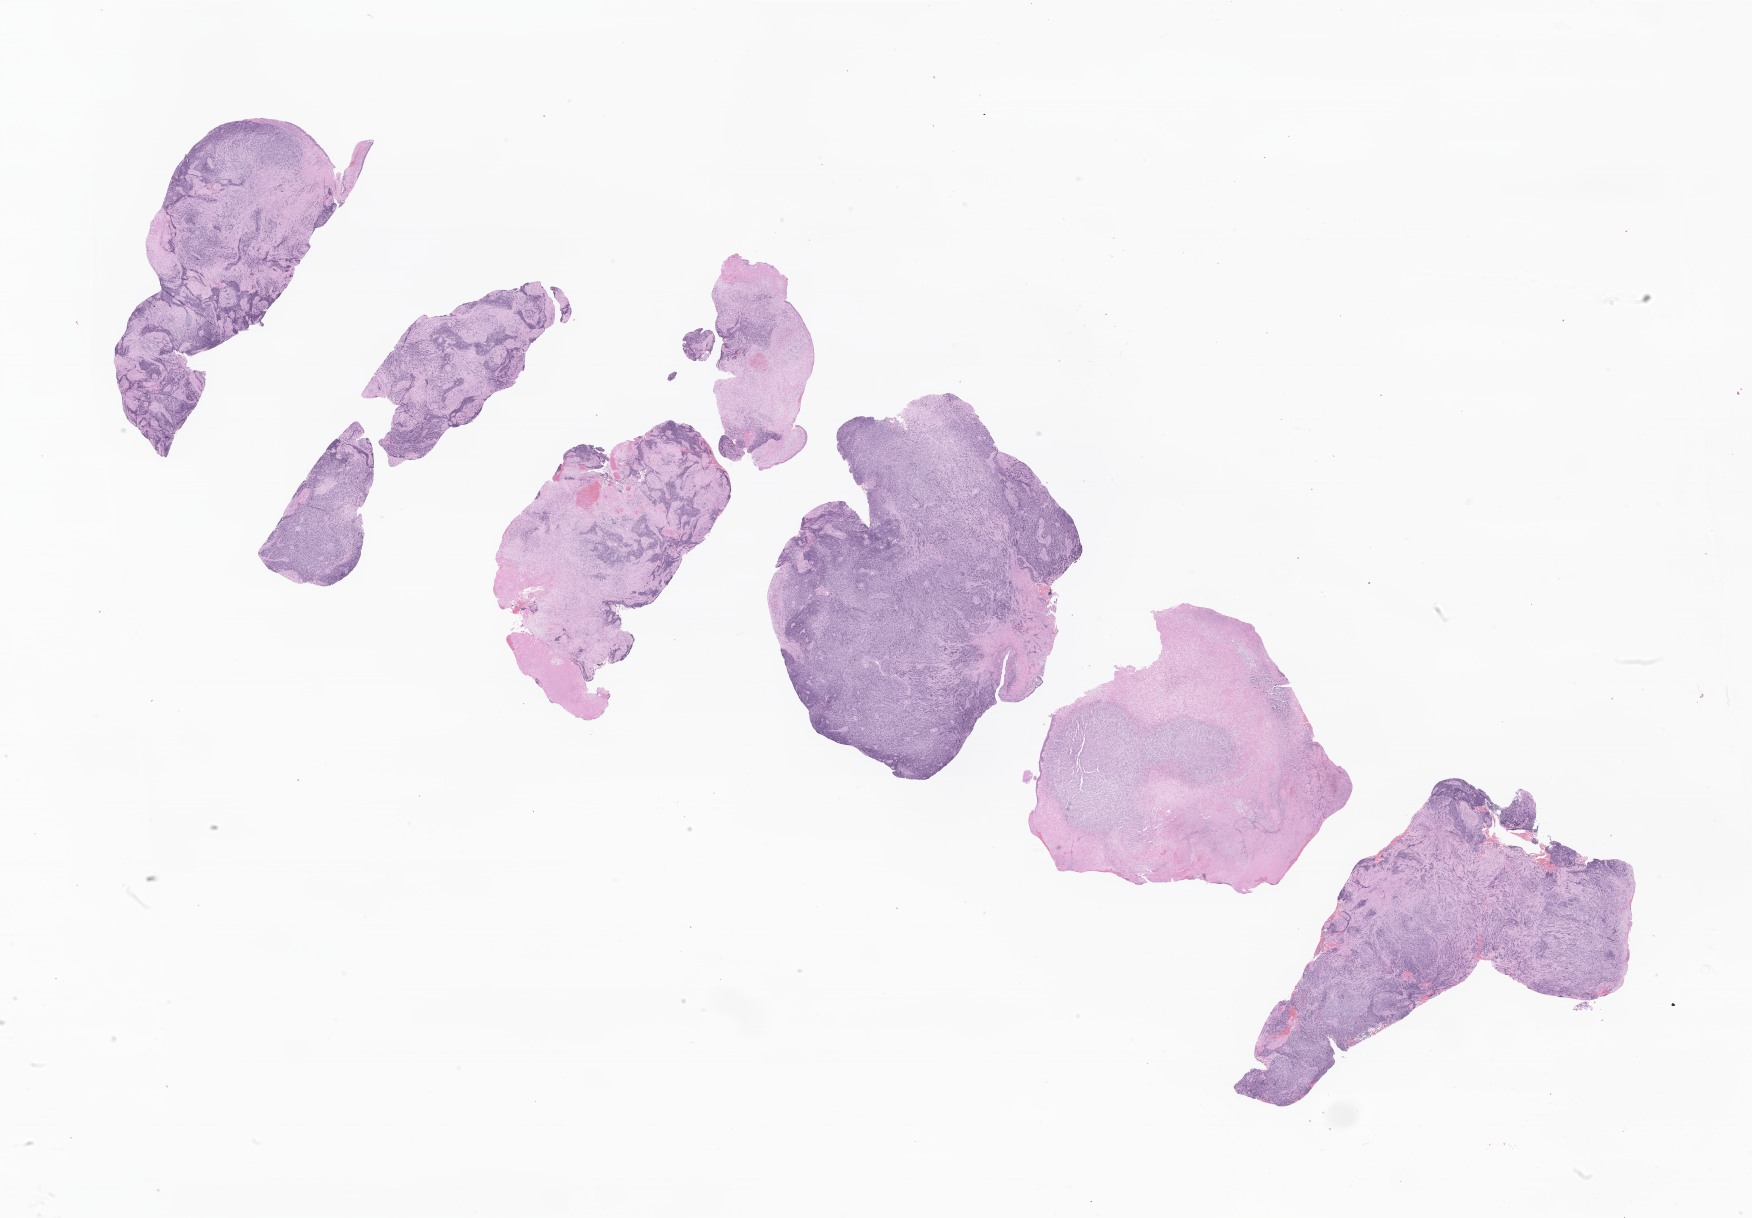
Haematoxylin and eosin whole-slide image of tumor tissue from the nasal cavity — shown as a low-resolution overview of the whole scanned area (about 29.6 x 20.5 mm); FFPE section. Female patient, age 221 months (18 years 5 months).
Recorded diagnosis: Alveolar rhabdomyosarcoma.